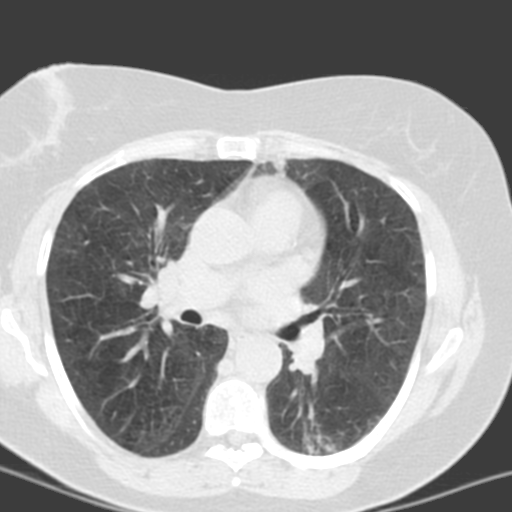
Chest CT (low-dose screening protocol), one axial image; third screening round (two years after baseline); lung window (W 1500 / L -600 HU); 120 kVp; slice 59 of 150 in the series. Female participant, aged 55 years at enrolment. Current smoker at enrolment.
Lesion marked by an expert reader, box from (x=288, y=412) to (x=366, y=464) px. The screening reader recorded 6 non-calcified nodules or masses ≥4 mm on this exam; which of them this box marks is not recorded. Participant outcome: lung cancer diagnosed 357 days after this screen — adenocarcinoma with mixed subtypes, left lower lobe, poorly differentiated (G3), stage IA (AJCC 6th edition), 21 mm at pathology.